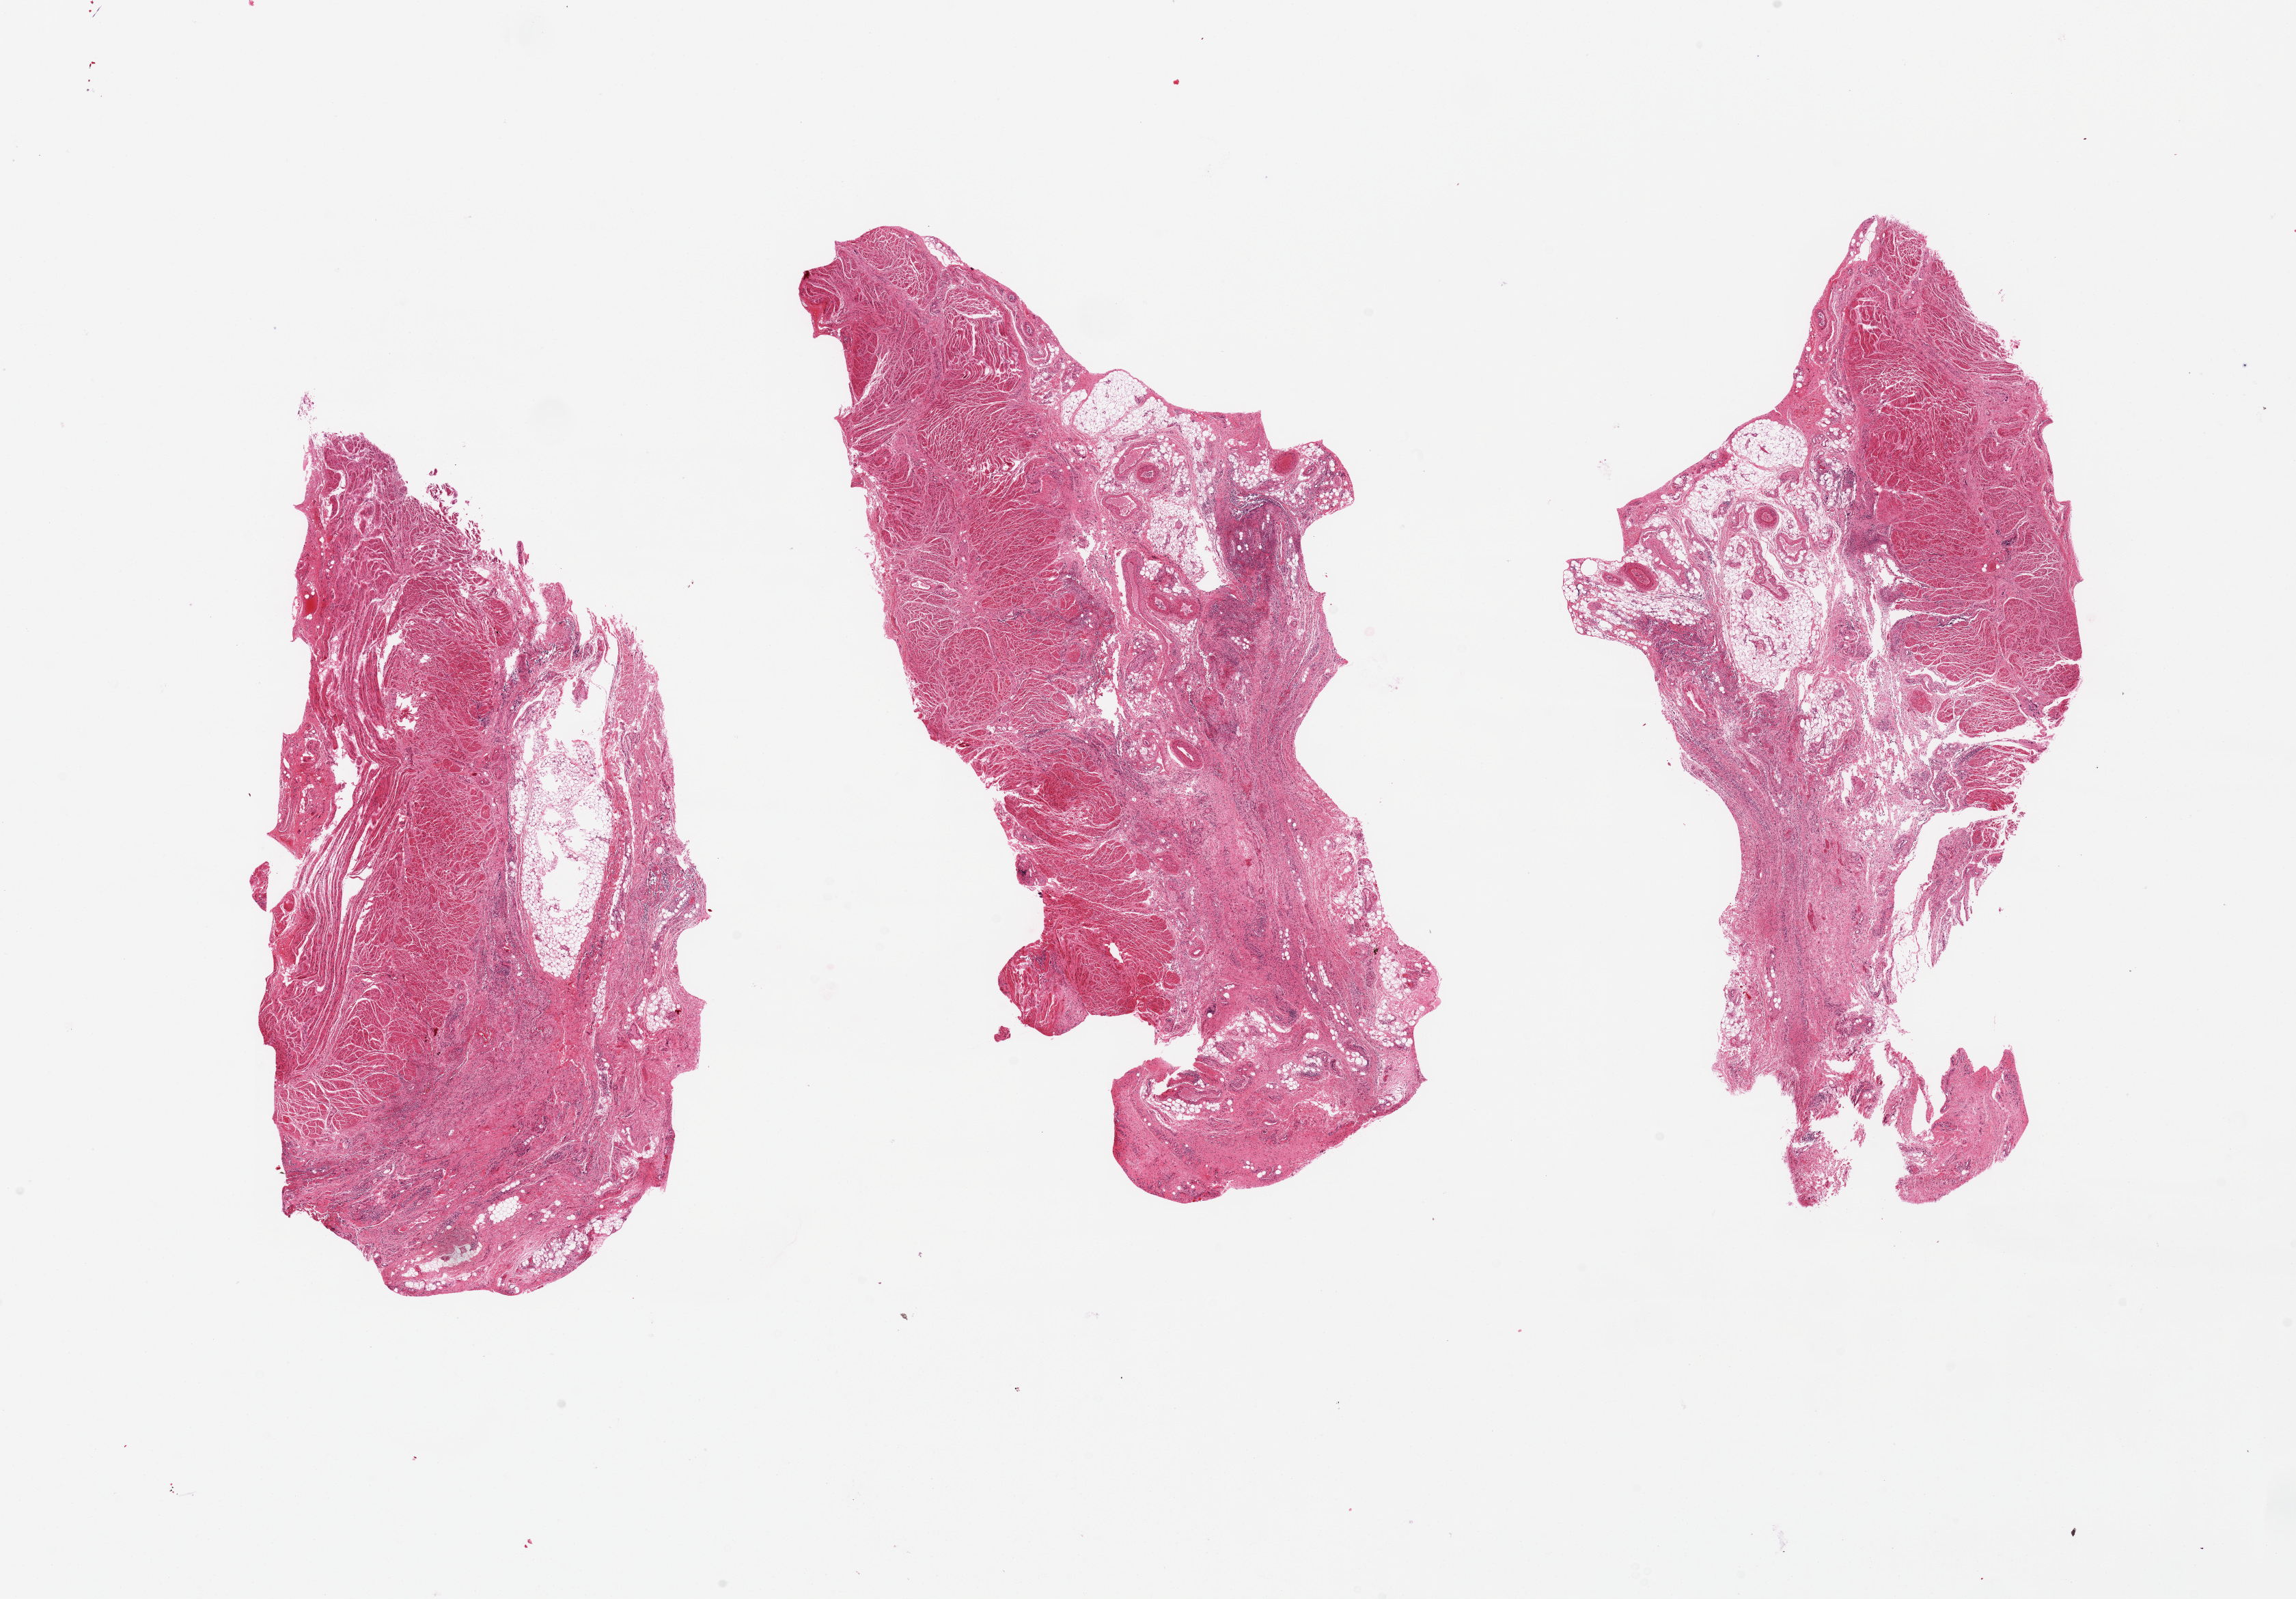
Whole-slide image, hematoxylin and eosin (H&E) stain — a low-resolution overview of the entire scanned area, about 26.6 x 18.5 mm; PAXgene-fixed, paraffin-embedded tissue; sampled site (target tissue): esophageal muscle; donor tissue sample. Donor: female.
Pathologist's review note for this sample: MUCOSA, NOT MUSCULARIS; 3 pieces 8.5x2 mm.